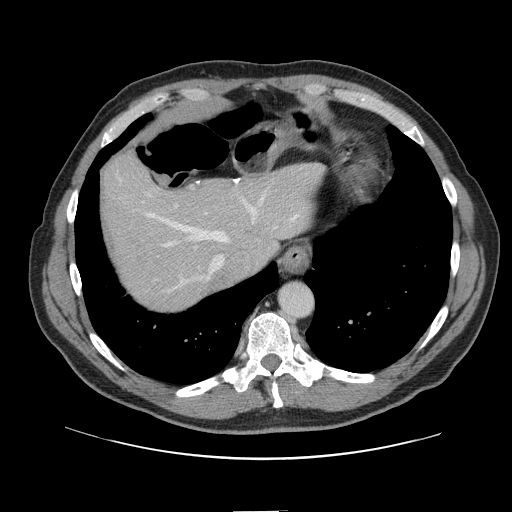
Contrast-enhanced abdominal CT, one axial slice. Slice 121 of 161 in the series (ordered by position). 120 kVp. Soft-tissue window (W 400 / L 40 HU). 2.5 mm slice thickness. 512 × 512 image matrix, field of view 412 × 412 mm. Male patient, age 66 years. Case-level facts recorded for this patient, not image findings: diagnosis: colorectal cancer liver metastases, imaged before liver resection; multiple liver metastases: no.
Structures marked on this image (outlined manually by an expert reader):
- hepatic veins: bounding box <119,179,299,292> (left, top, right, bottom; pixels)
- liver: <101,156,318,310>
- planned liver remnant (the part of the liver to remain after resection): <101,155,318,298>
- liver metastasis: <200,273,227,295>